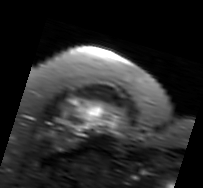
MRI of an extremity soft-tissue mass, one axial slice. Position 63 of 91 along the scan axis. T2-weighted fat-saturated. MR volume resampled by the dataset authors to the PET/CT grid (not the native acquisition matrix). 3.27 mm slice thickness. 203 × 188 image matrix, field of view 198 × 184 mm. Female patient. Case-level facts recorded for this patient, not image findings: histological type: malignant solitary fibrous tumor; grade: intermediate; site of the primary tumour: right thigh.
Annotated regions visible in this slice (expert contour drawn on MRI and transferred to this co-registered scan by the dataset authors):
- gross tumour volume including surrounding oedema: bounding box [x1, y1, x2, y2] px = [56, 95, 127, 148]
- gross tumour volume (mass): [78, 99, 111, 130]